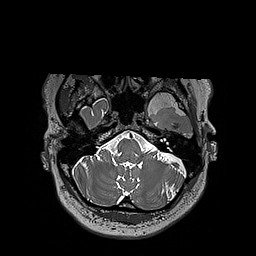
Brain MRI from a brain-tumour surgery series, one axial slice. 1 mm slice thickness. 256 × 256 image matrix, field of view 250 × 250 mm. Case-level facts recorded for this patient, not image findings: histopathology: Oligodendroglioma; WHO grade: 3.
Annotated regions visible in this slice (expert manual segmentation):
- tumour: bounding box [x1, y1, x2, y2] px = [124, 92, 197, 113]